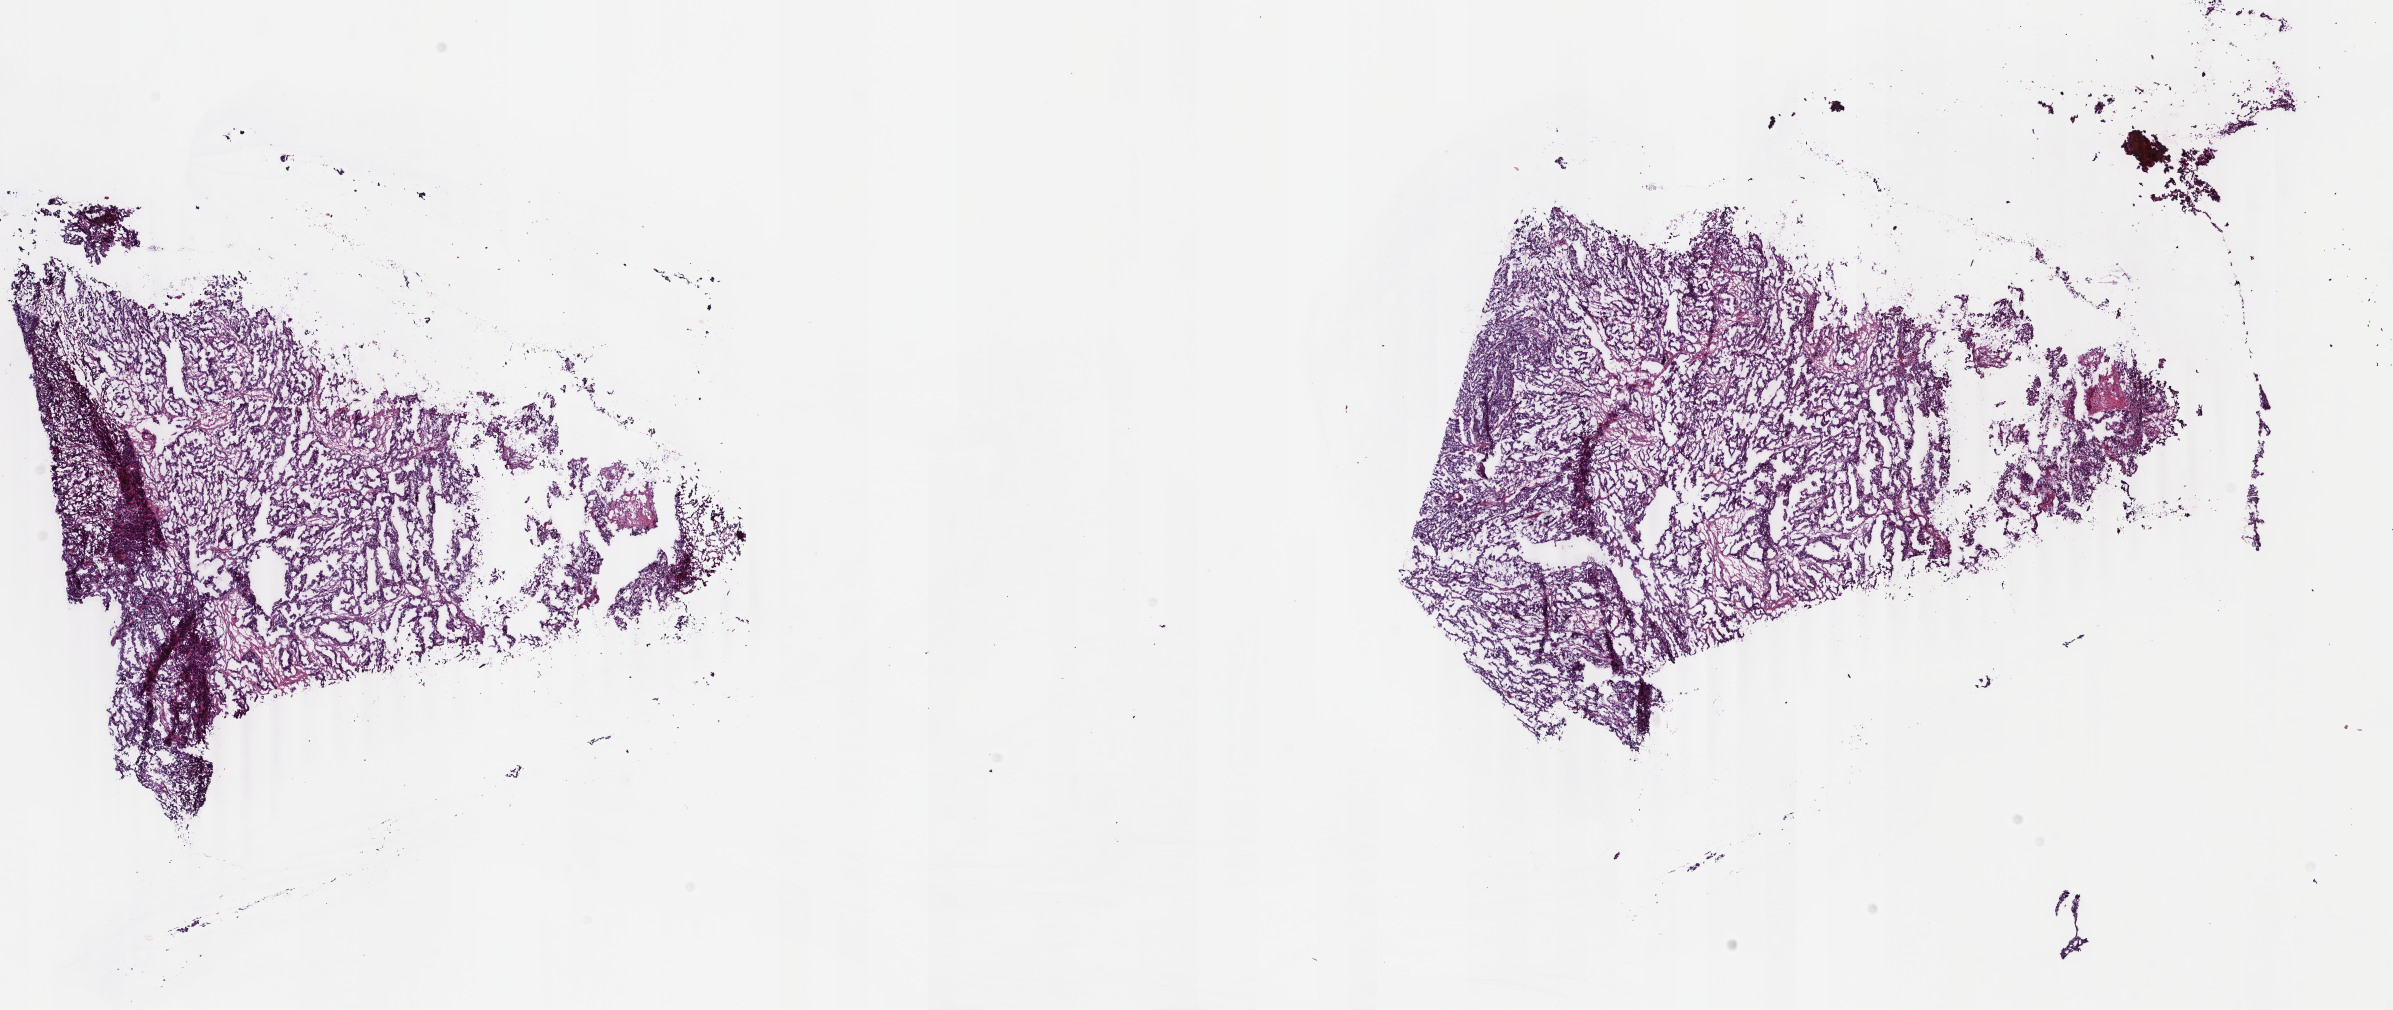
Whole-slide histology image, Hematoxylin and eosin (H&E) stained — a low-resolution overview of the entire scanned area, about 19.0 x 8.0 mm (acquisition: 40x scan), frozen section, sample: primary tumour, uterus. Female patient; age at initial diagnosis 59 years. Histologic grade: G3 (poorly differentiated). Pathologist review of this section (percent, as recorded): tumour cells 75%, tumour nuclei 90%, normal cells 0%, stromal cells 20%, necrosis 5%. Inflammatory infiltration, as recorded: lymphocyte infiltration 1%, monocyte infiltration 1%, neutrophil infiltration 0%.
• FIGO stage: IVB
• pathologic diagnosis: Serous cystadenocarcinoma, NOS (endometrium)